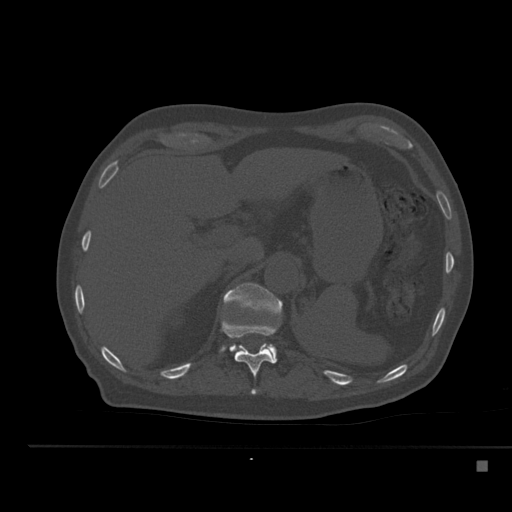
CT including the spine, one axial slice. Position 244 of 517 along the scan axis. Reconstruction kernel Br40s. Bone window (W 1800 / L 400 HU). 1.5 mm slice thickness. 512 × 512 image matrix, field of view 408 × 408 mm. Male patient, age 70 years. From the clinical record (not read from this slice): primary cancer: renal; vertebrae with lytic lesions (as recorded): T4, T6, T10, T12, L3, L4, L5.
Annotated regions visible in this slice (semi-automatic segmentation, software-assisted and operator-edited):
- T11 vertebra: bounding box [x1, y1, x2, y2] px = [222, 319, 277, 395]
- T12 vertebra: [223, 283, 283, 363]